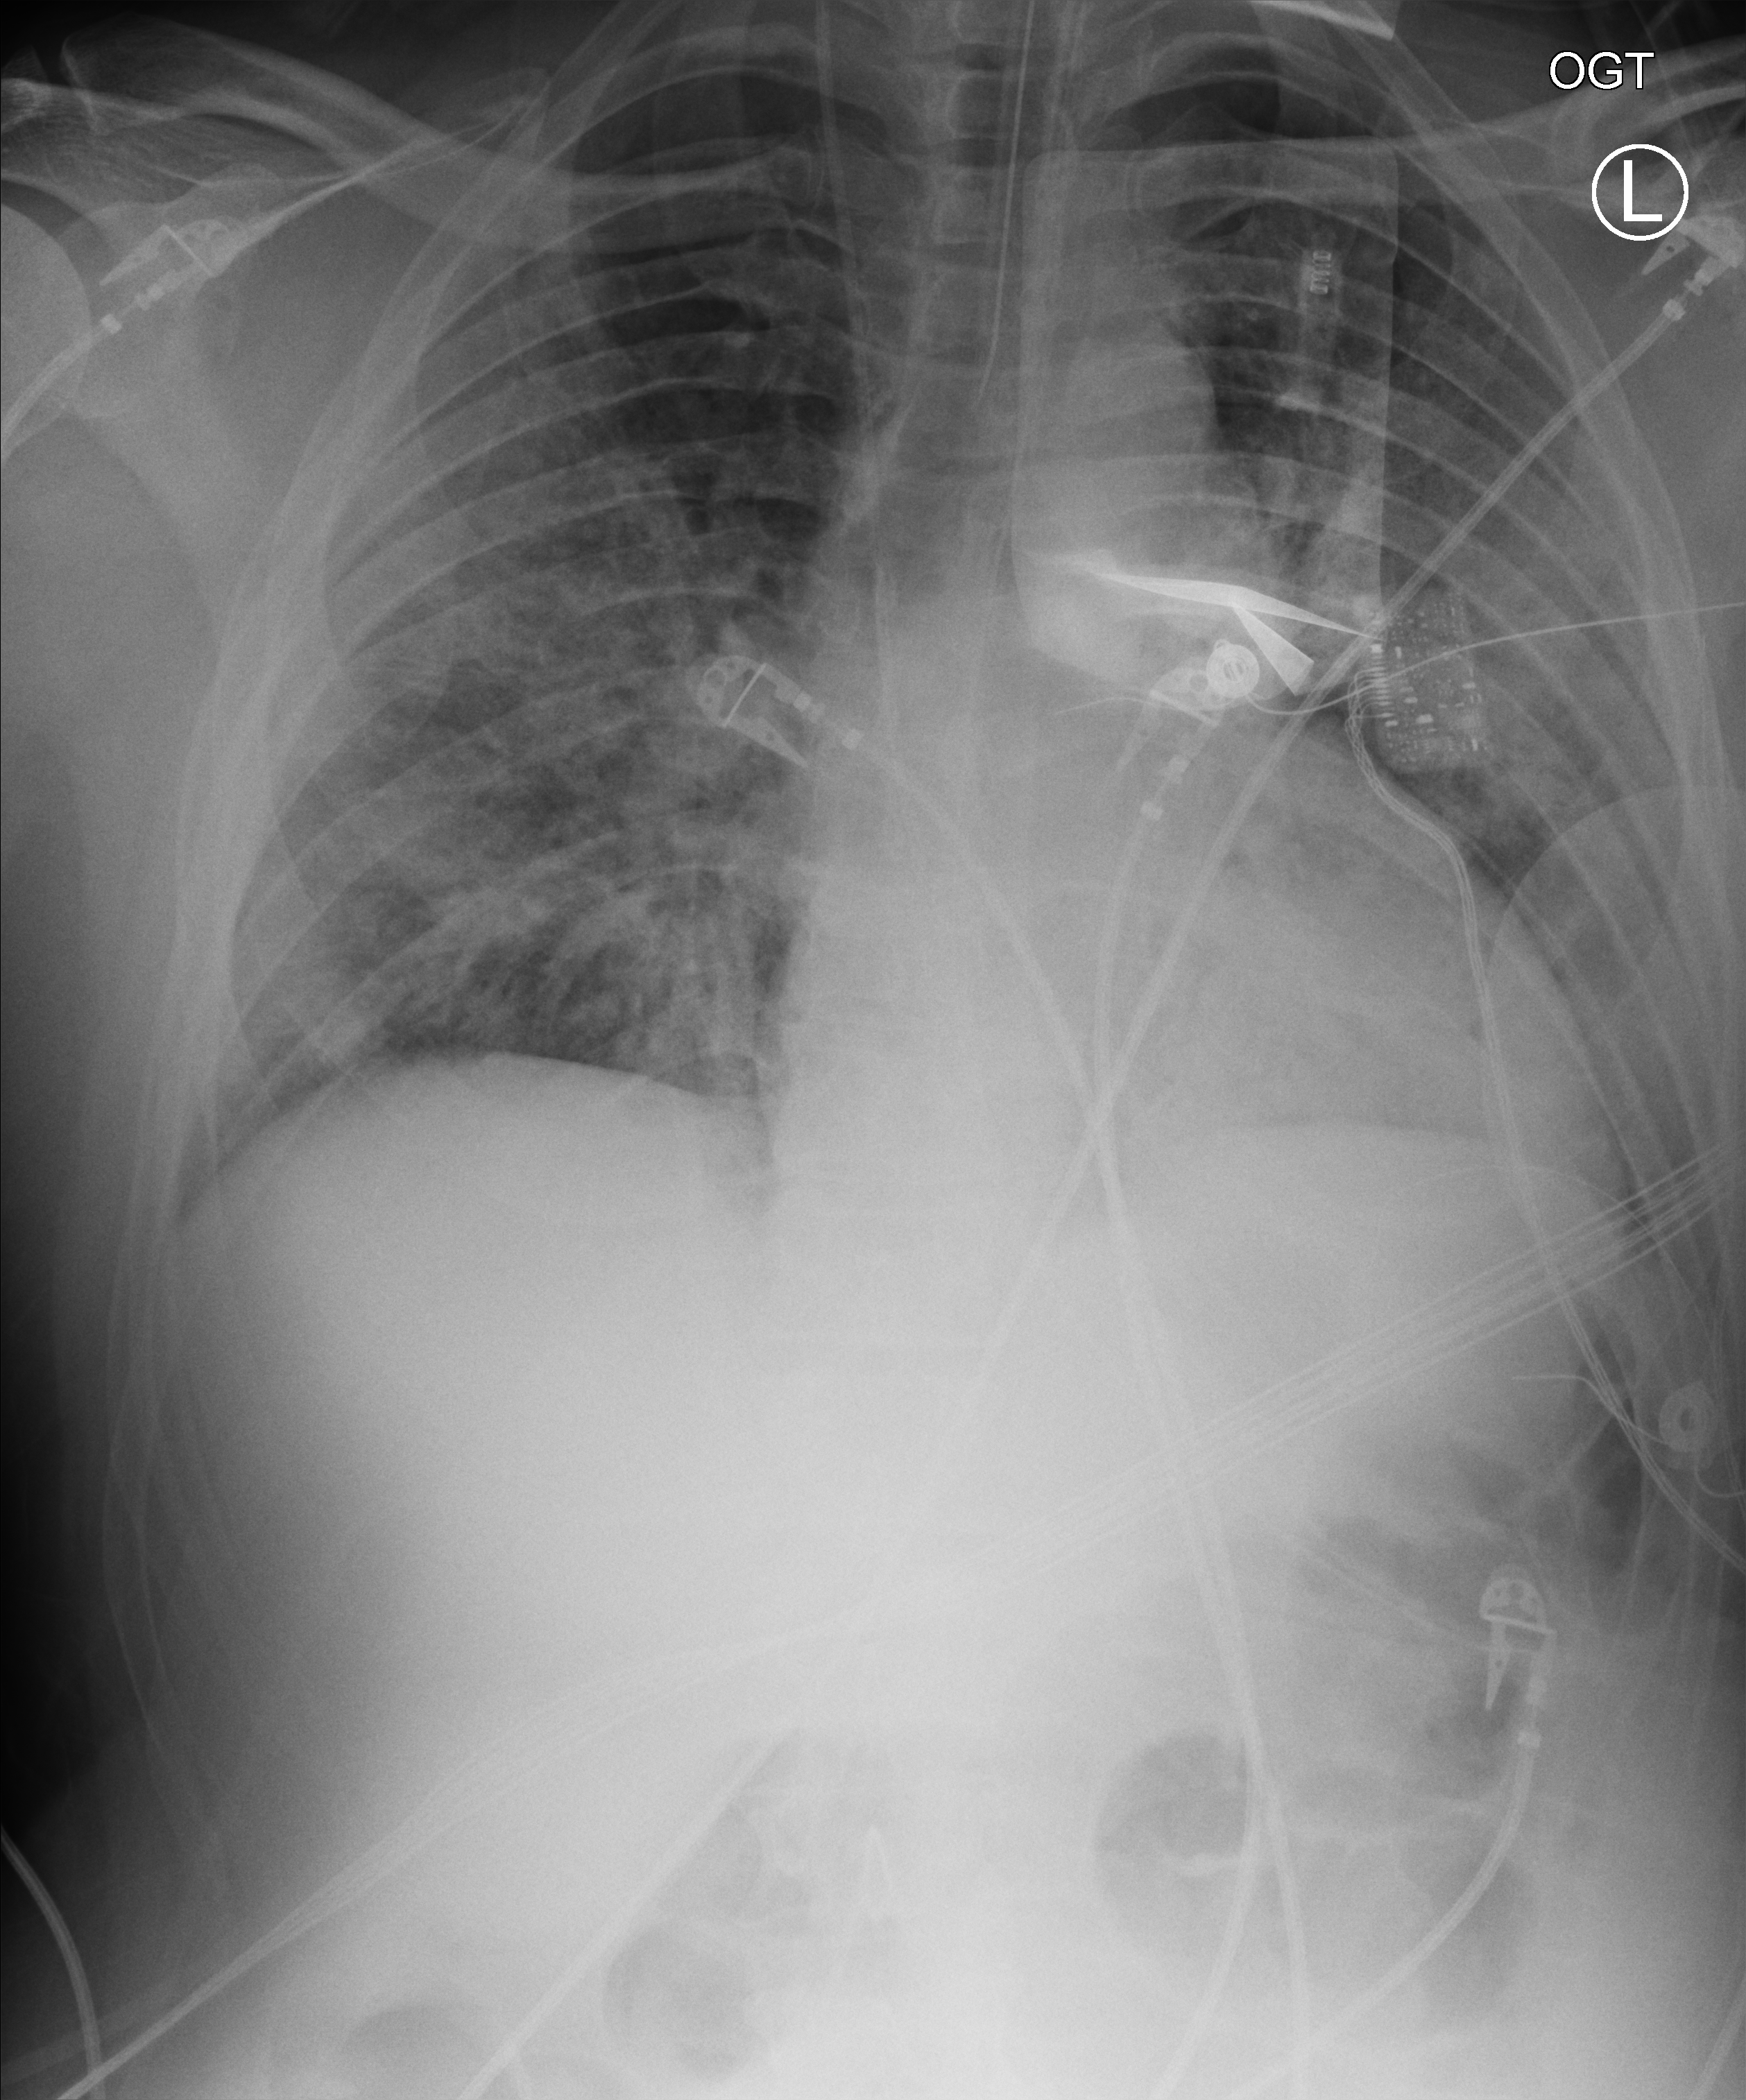
Bedside chest radiograph (computed radiography), anteroposterior (AP) projection. Male patient hospitalised with COVID-19, age 18–59 years.
Hospital-stay facts (about this admission, not read from this image; timing relative to this image not recorded):
- diabetes (admission record): no